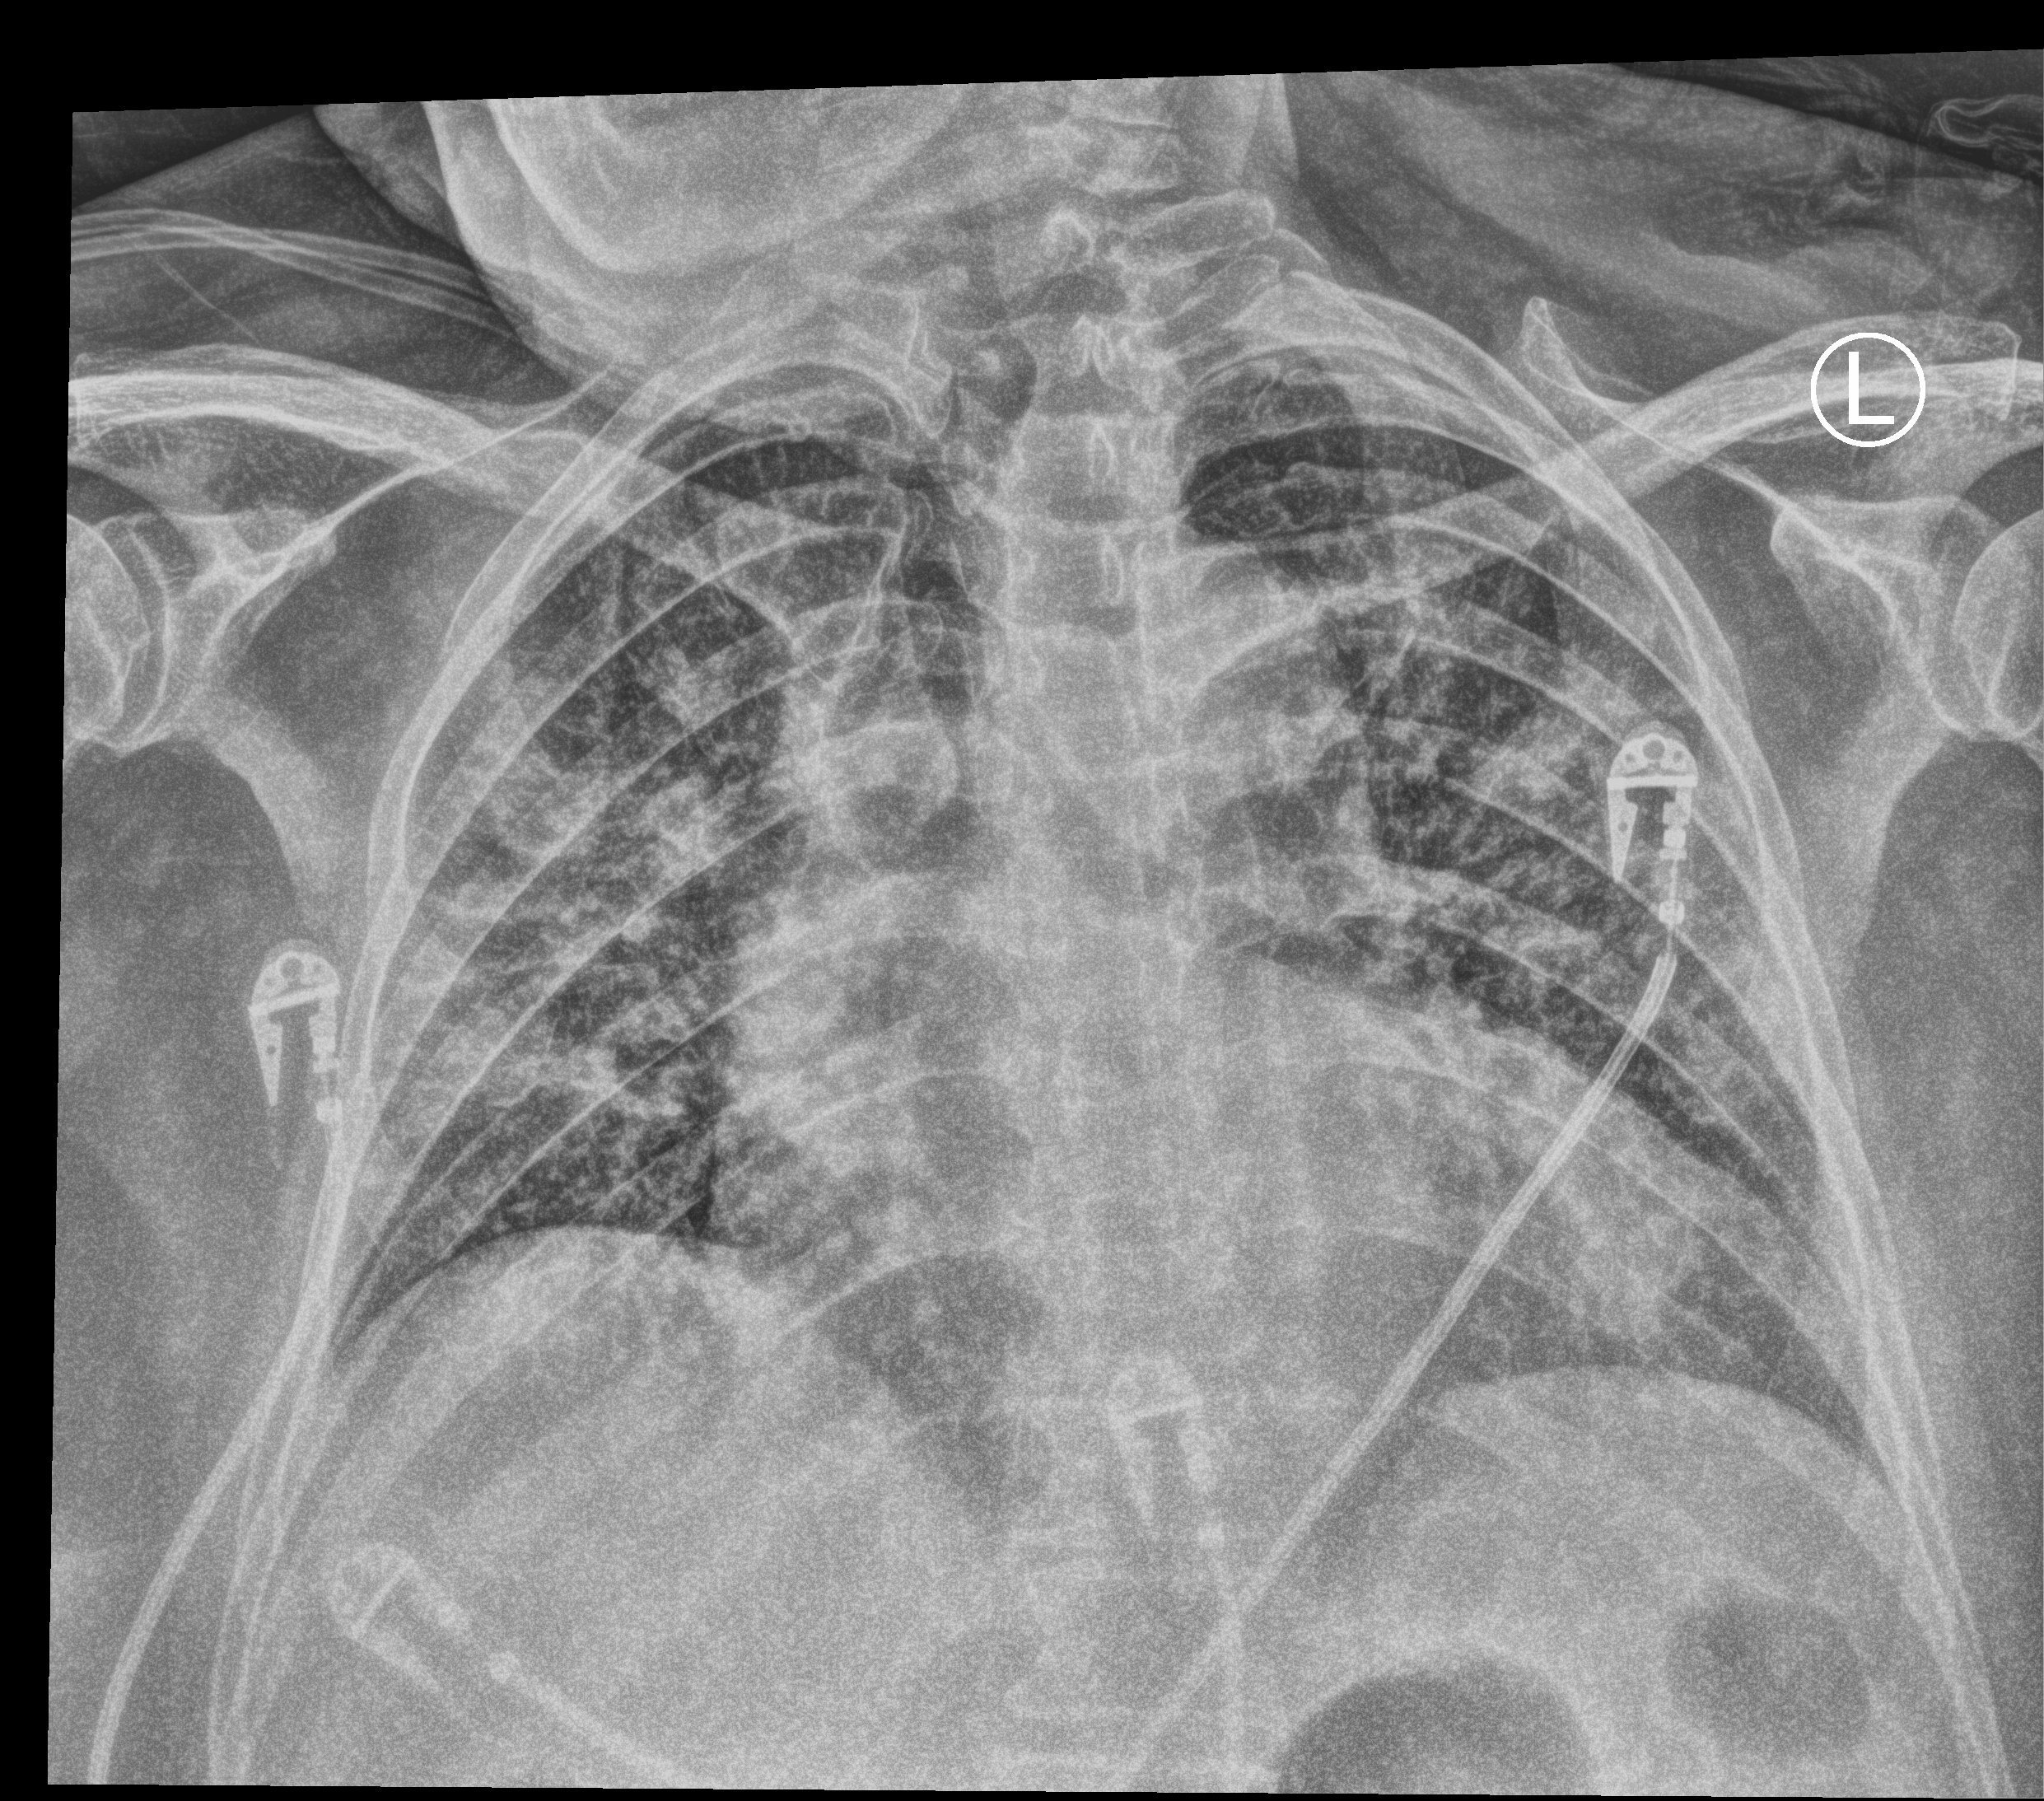
Portable chest radiograph; anteroposterior (AP) projection. Patient hospitalised with COVID-19; female, aged 60–74 years.
Admission-level facts for this patient (not findings on this image; timing relative to this image not recorded): chronic kidney disease (admission record): no.